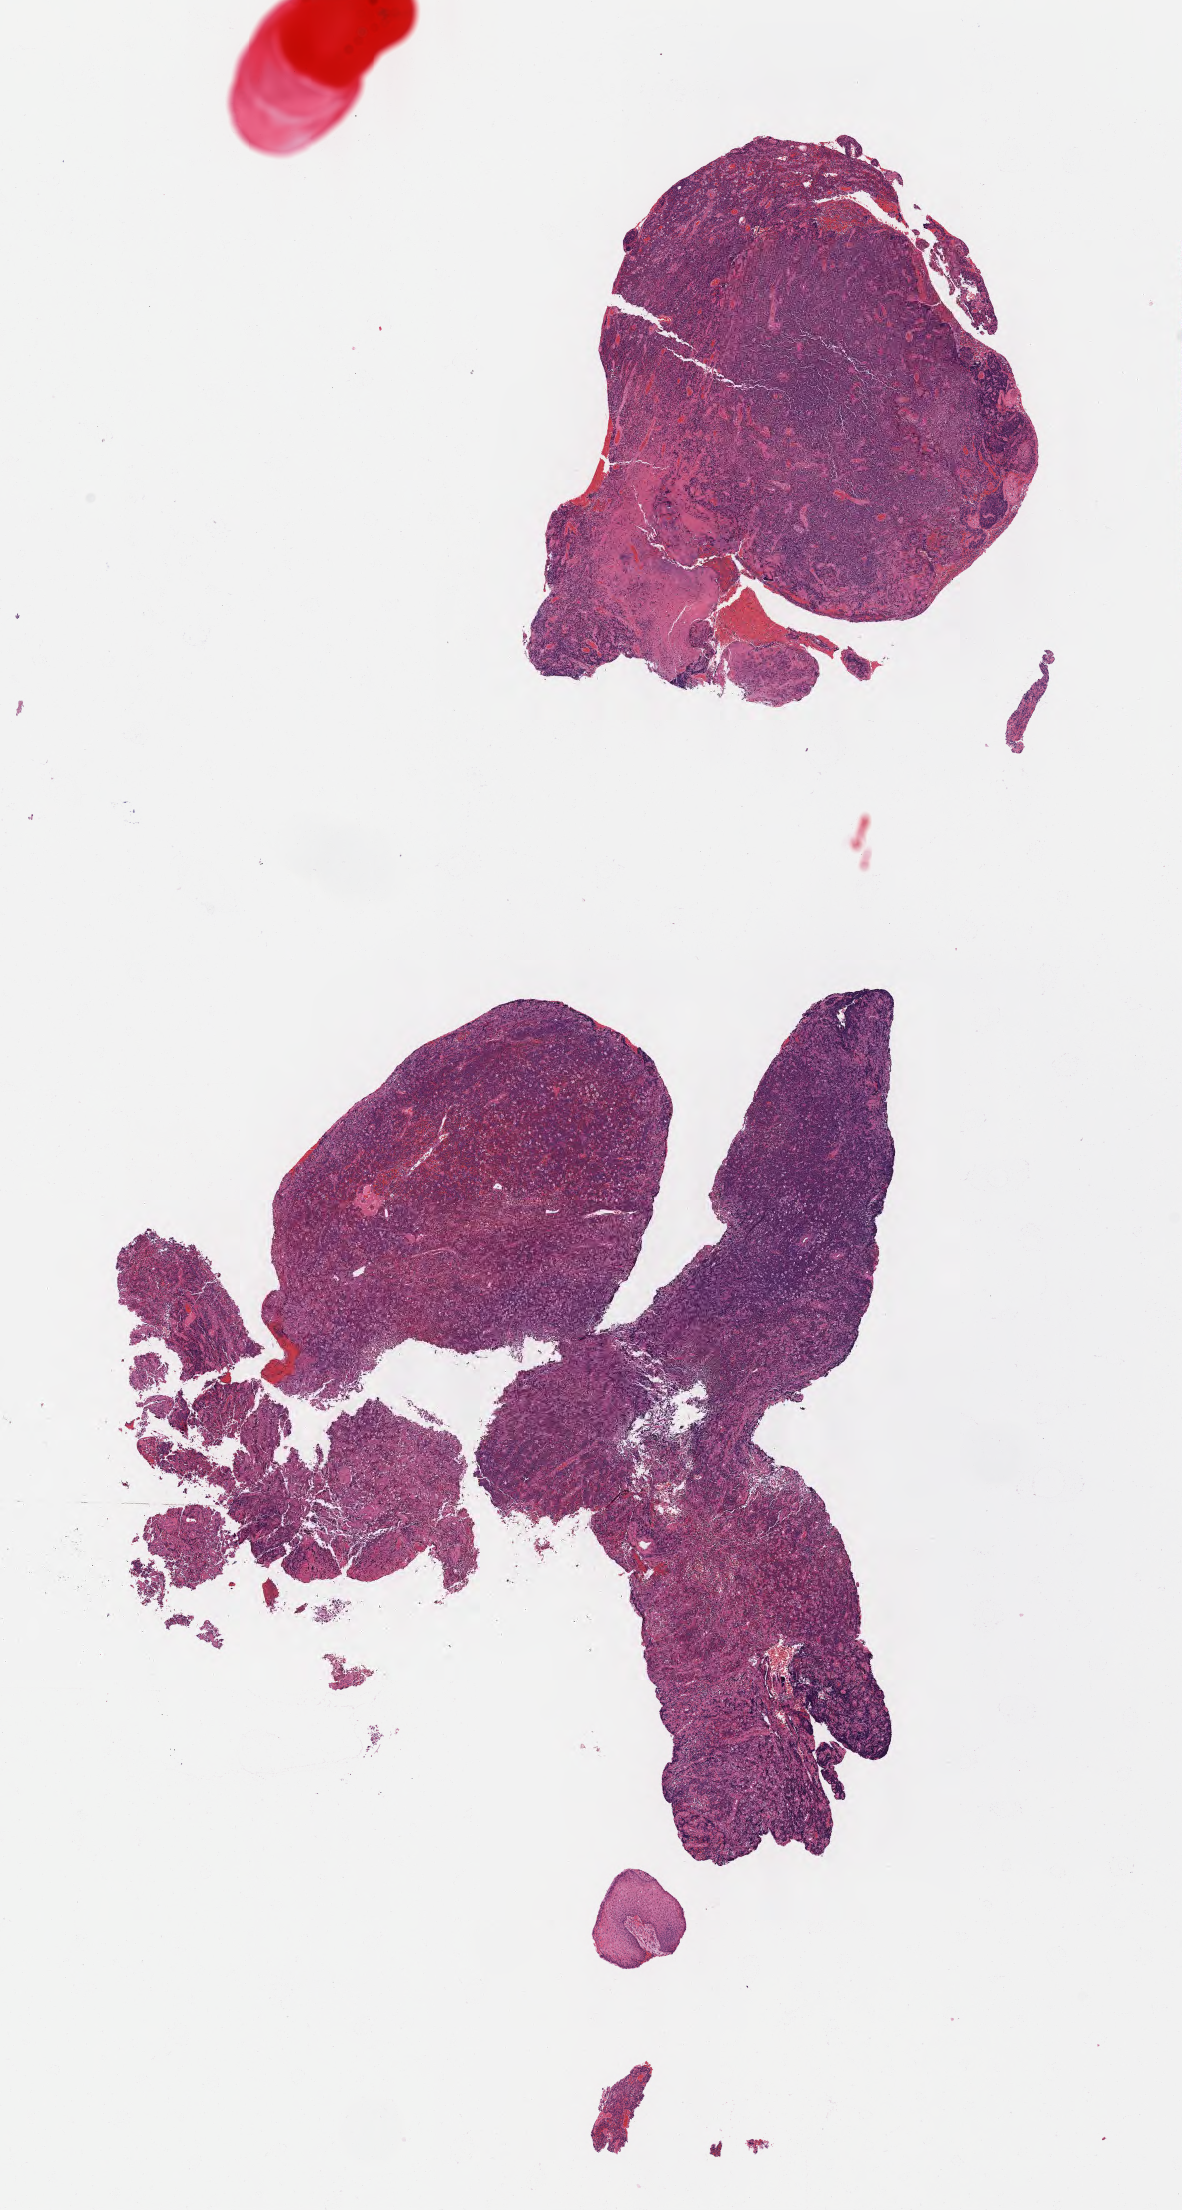
Whole-slide image, H&E stain, shown as a low-resolution overview of the whole scanned area (about 9.6 x 17.9 mm); FFPE section; primary tumor; anatomic site: cranium. Male, age 5 years at initial diagnosis. Composition of this section per pathologist review: tumor cells 85%, tumor nuclei 95%, stromal cells 5%, necrosis 10%, normal cells 0%. Infiltration values recorded for this section: lymphocyte infiltration 30%, monocyte infiltration 30%, neutrophil infiltration 5%.
Diagnosis: Burkitt lymphoma, NOS. Ann Arbor stage (patient): Stage II. Section: top of the tissue portion.